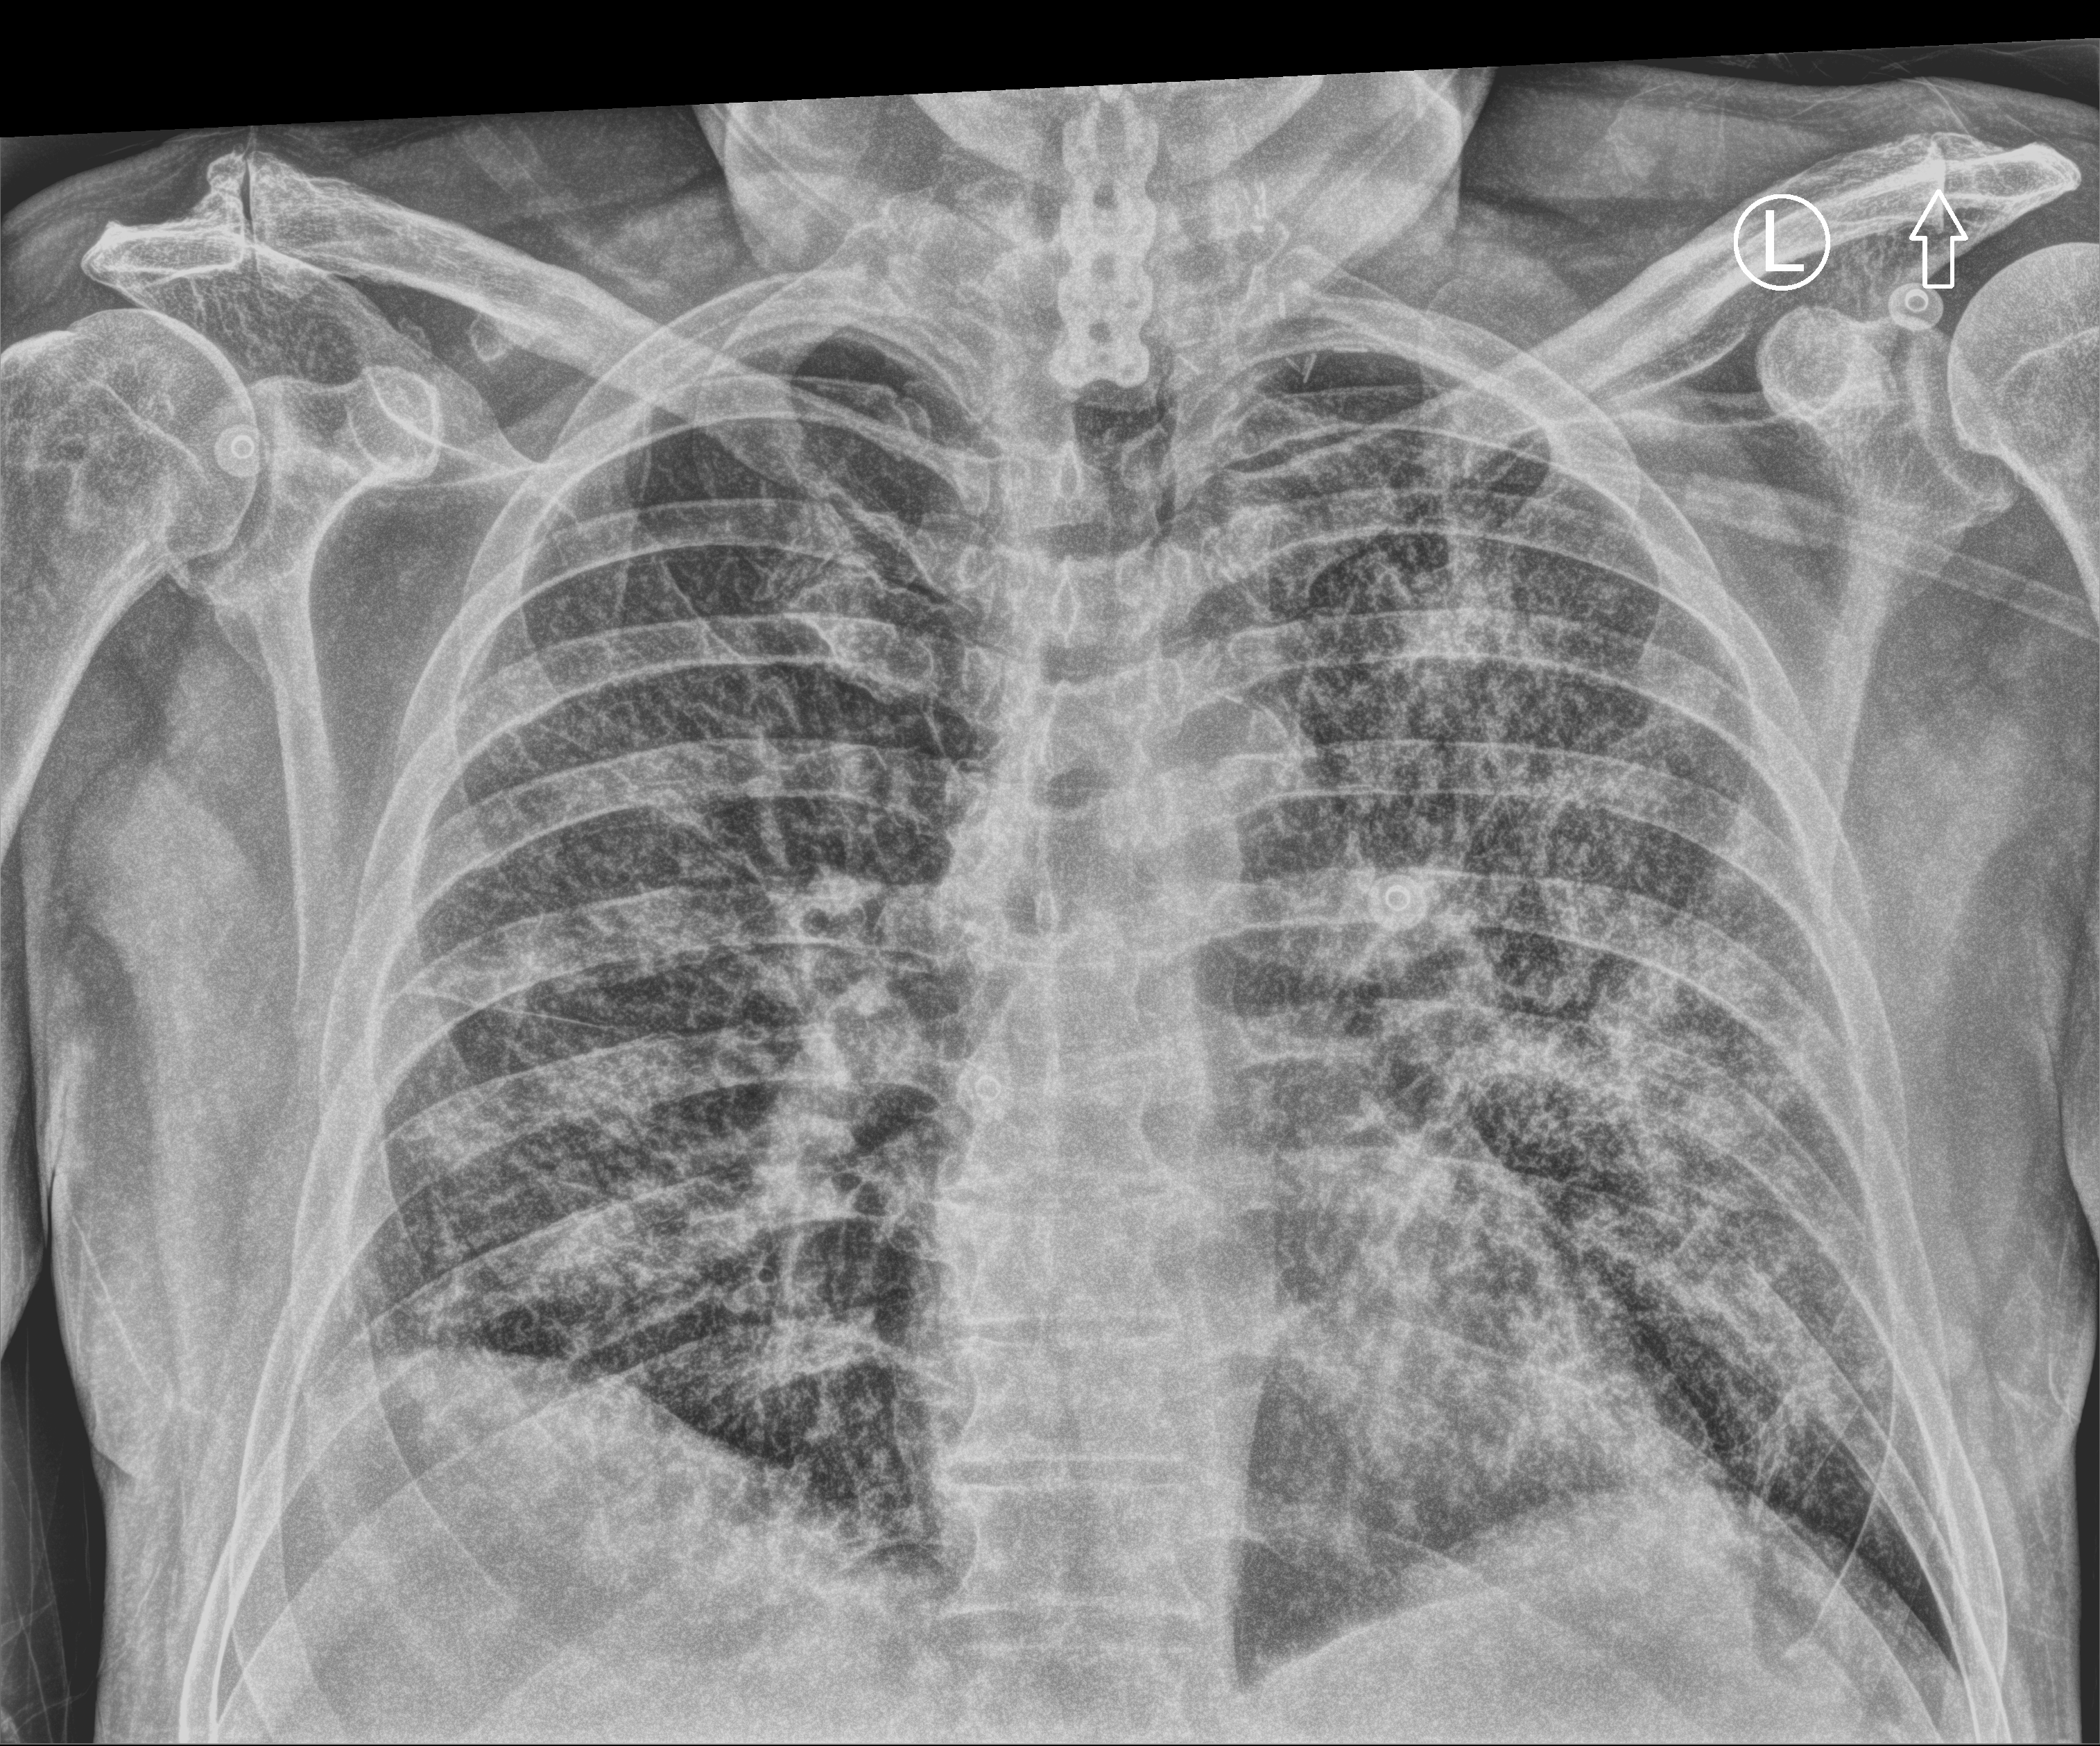
Chest X-ray (portable), anteroposterior (AP) projection. Male patient hospitalised with COVID-19, age 60–74 years.
Hospital-stay facts (about this admission, not read from this image; timing relative to this image not recorded): length of hospital stay: 43 days; admitted to intensive care during this hospital stay: yes.